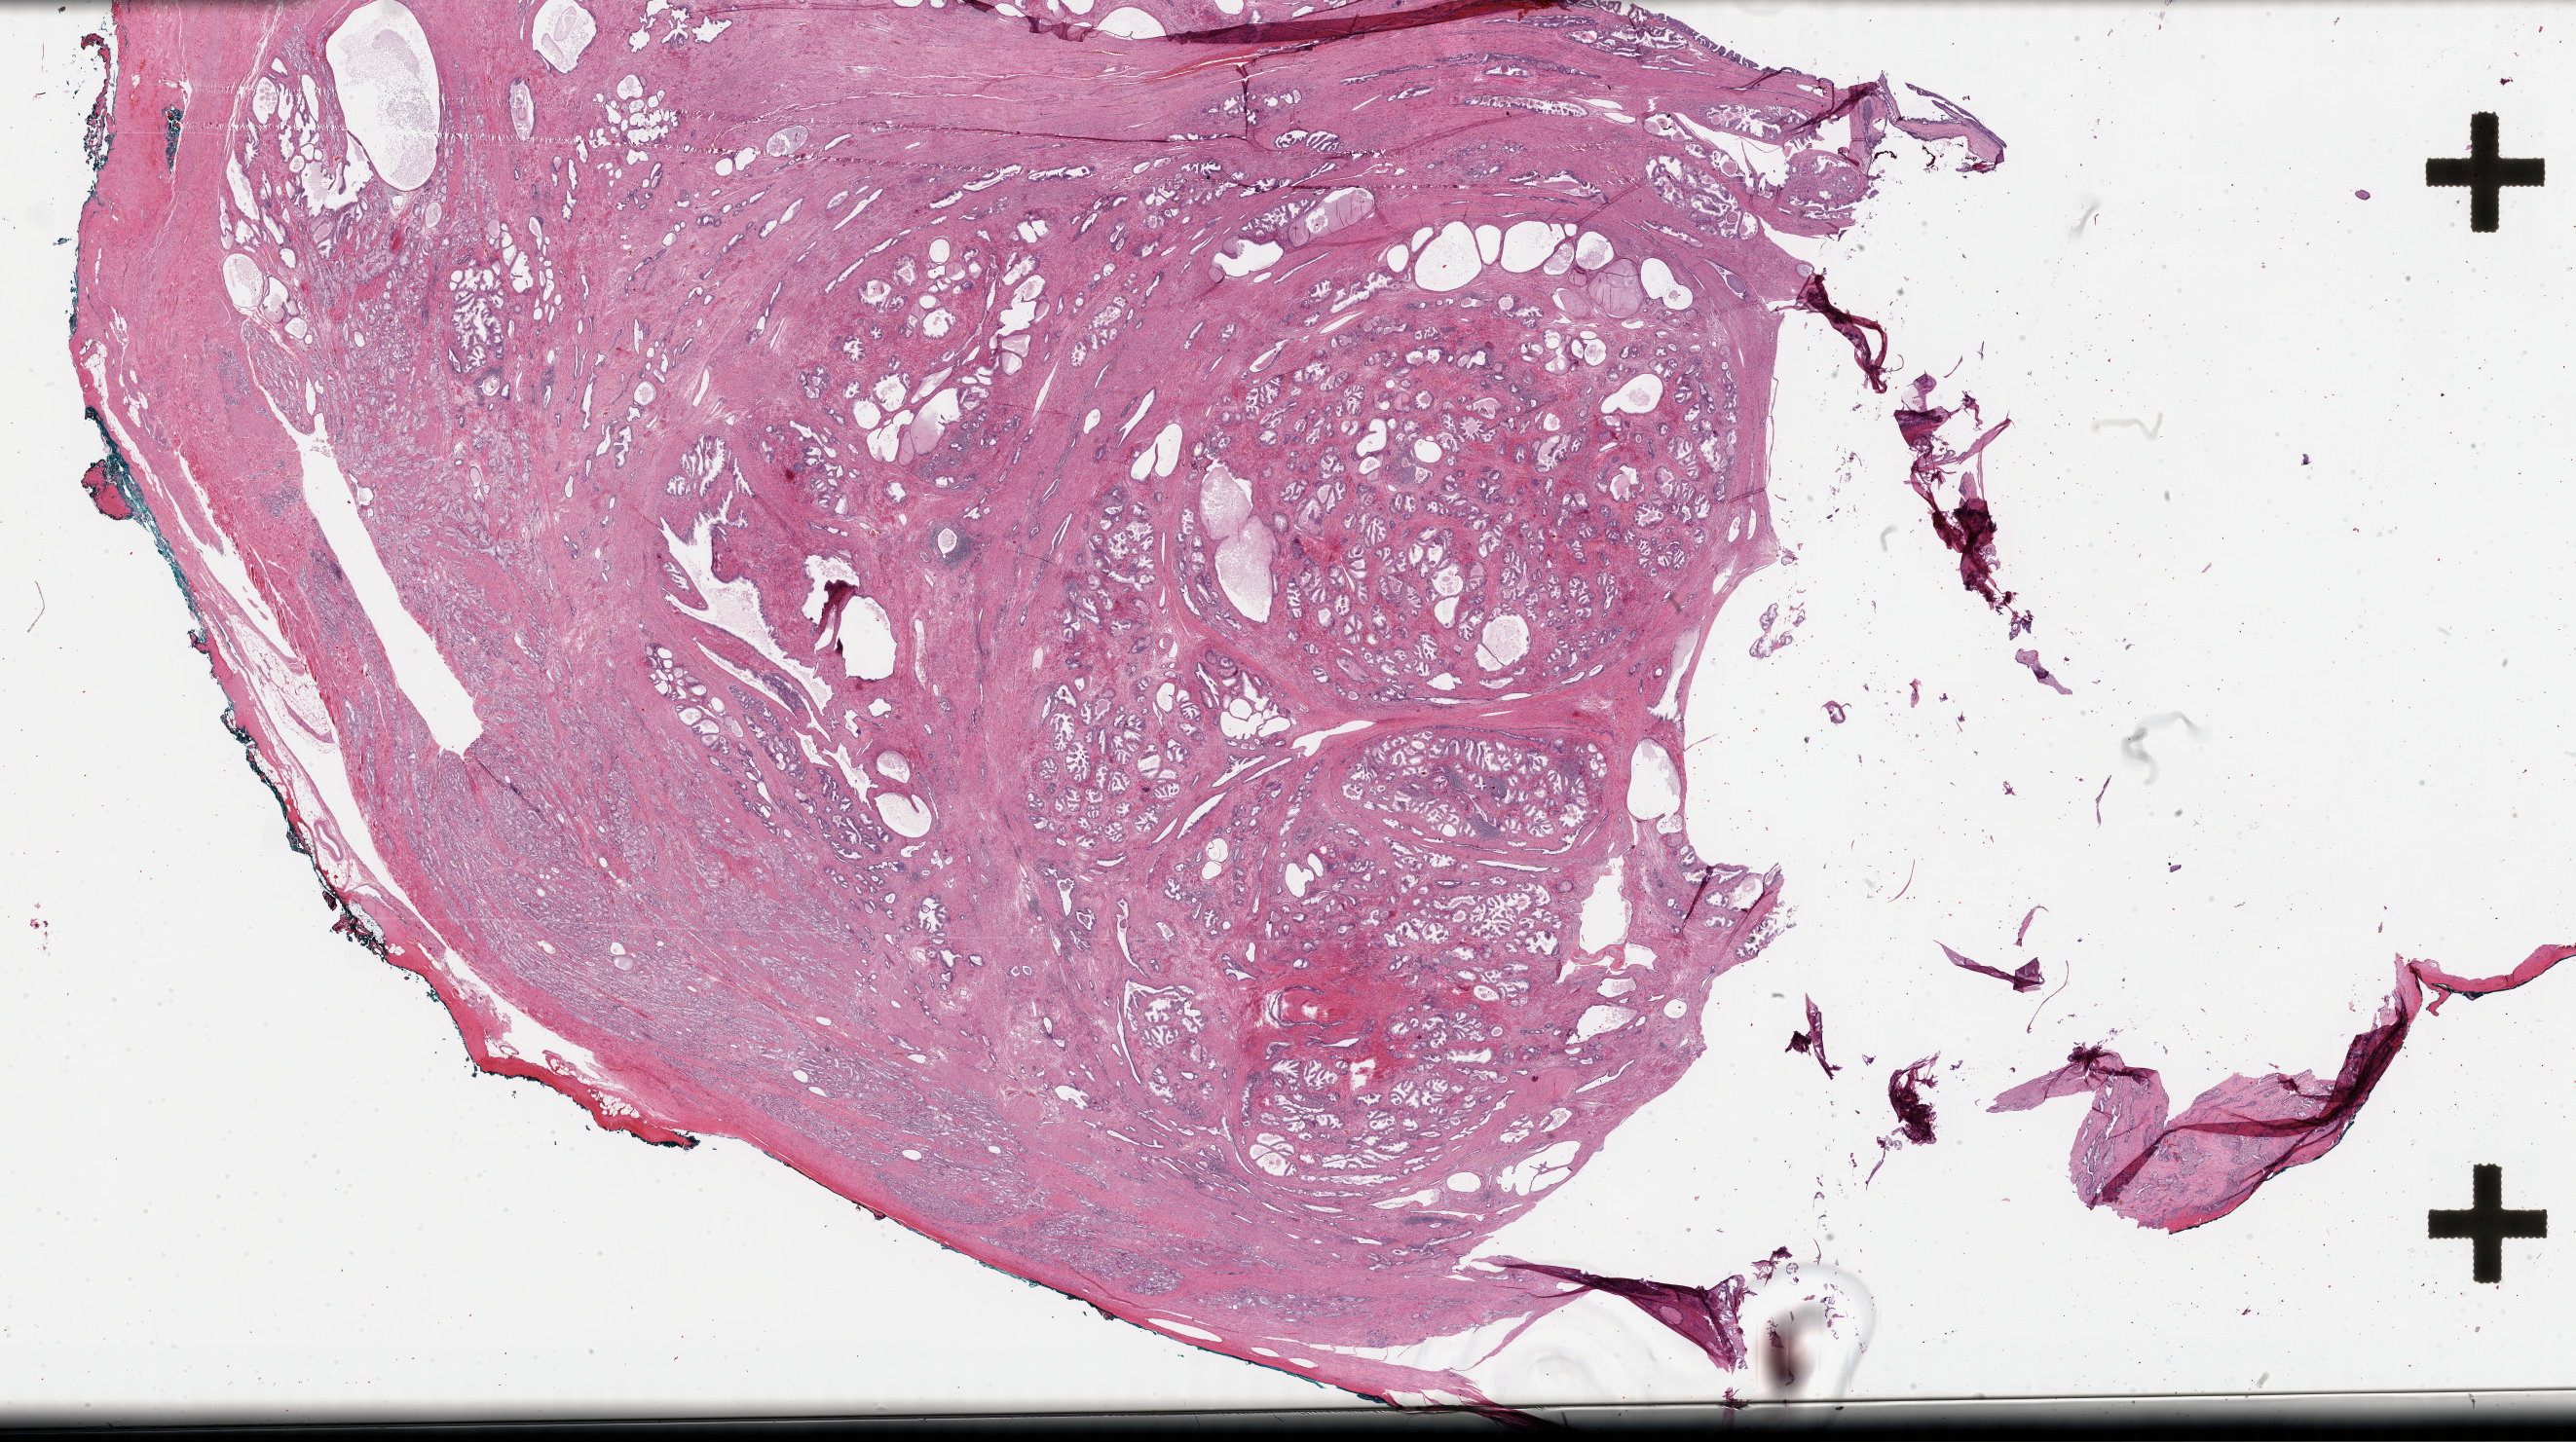
Whole-slide histology image, H&E-stained, whole scanned area (about 42.8 x 24.0 mm) shown as a low-resolution overview, formalin-fixed paraffin-embedded (FFPE) diagnostic section, sample: primary tumour, prostate. Patient: male, age at initial diagnosis 57 years.
Histologic diagnosis: Adenocarcinoma, NOS (prostate gland).